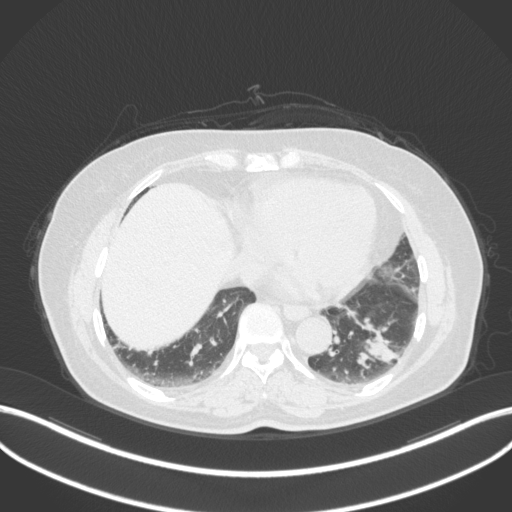
Chest CT, one axial slice. Slice 121 of 307 in the series (ordered by position). 120 kVp. Lung window (W 1500 / L -600 HU). 1 mm slice thickness. 512 × 512 image matrix. Female patient, age 59 years. Case-level facts recorded for this patient, not image findings: clinical TNM (as recorded): T2a N0 M0; histopathological grade: G2-3.
Structures marked on this image (bounding box drawn by a radiologist):
- lung tumour (recorded histology: adenocarcinoma): bounding box <348,309,401,371> (left, top, right, bottom; pixels)